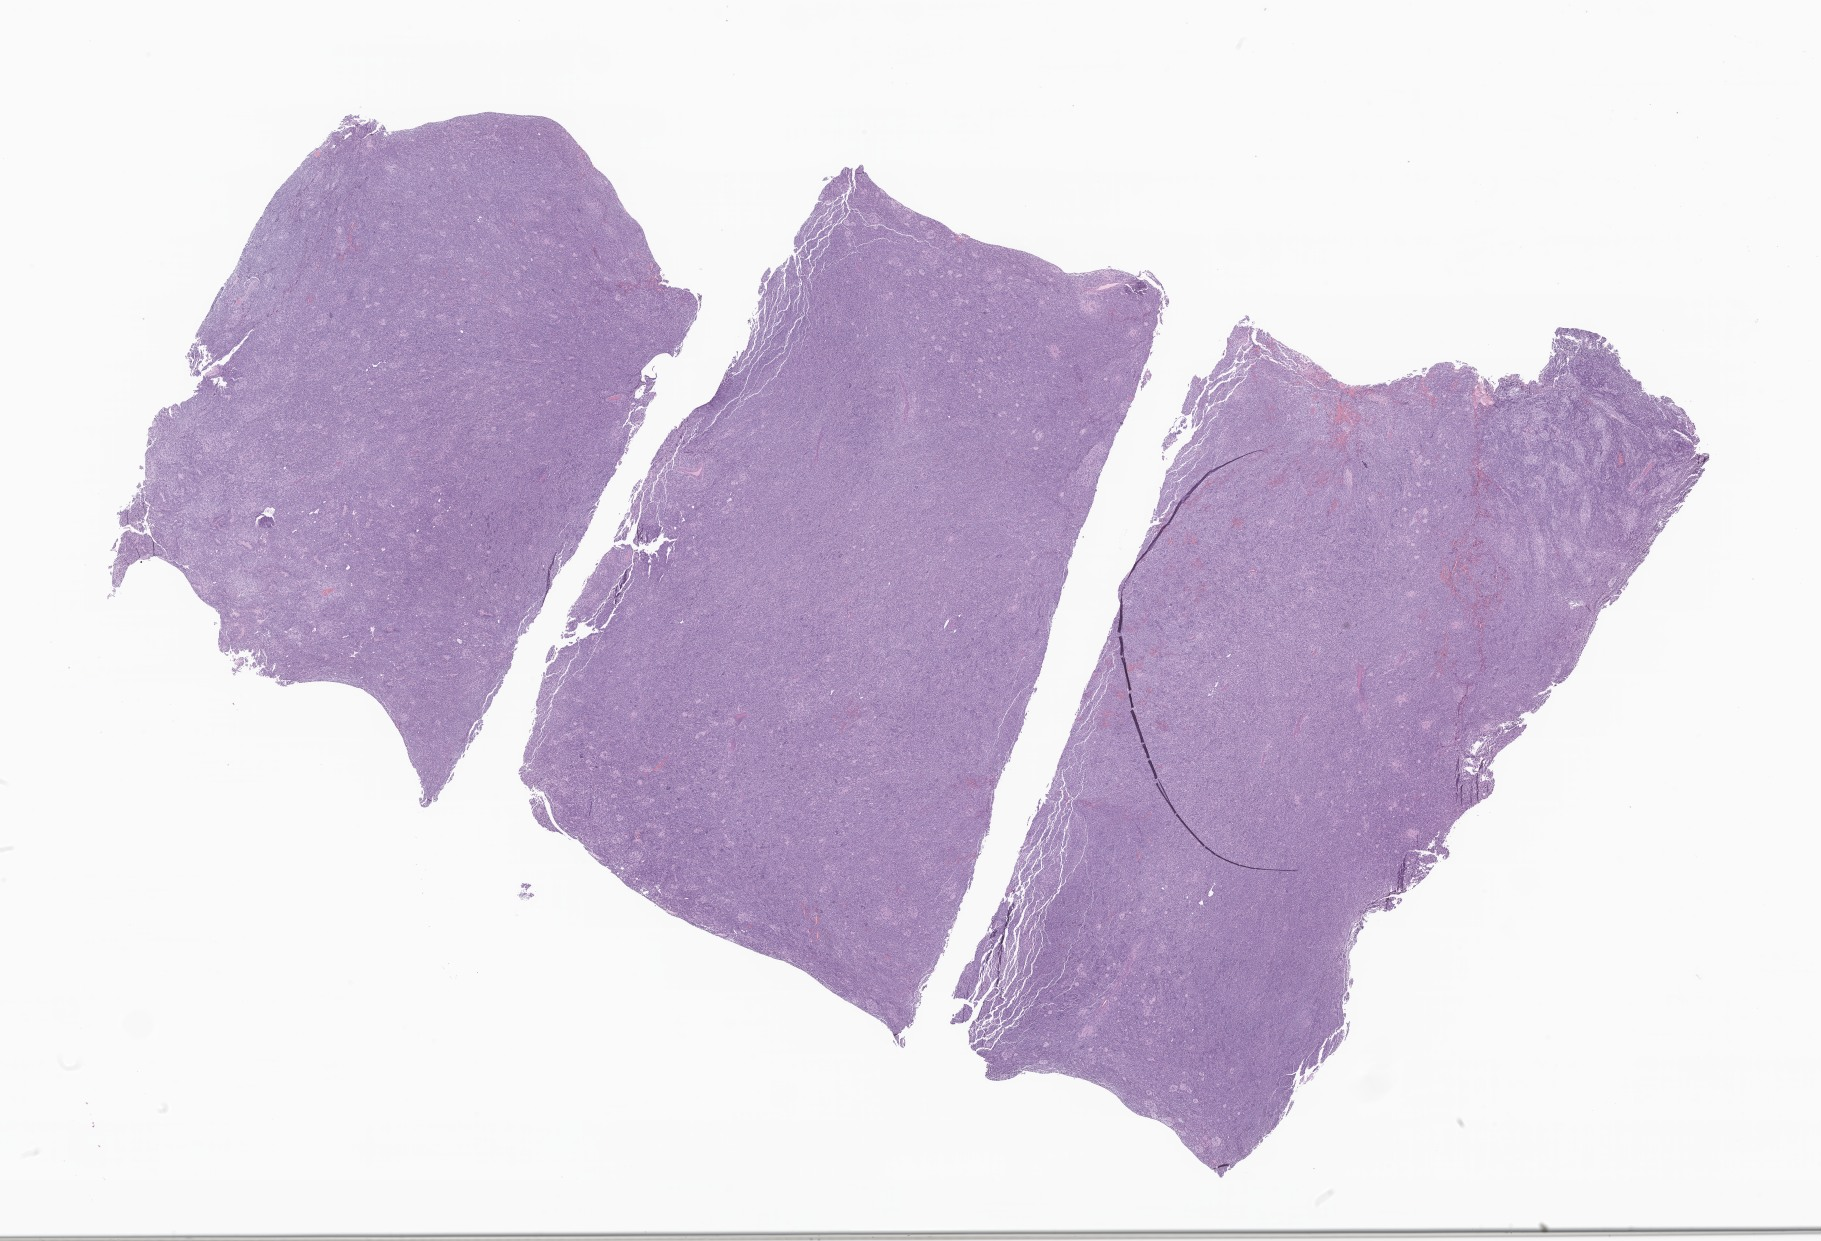
Whole-slide image, H&E stain of tumor tissue from the brain, shown as a low-resolution overview of the whole scanned area (about 30.7 x 20.9 mm); formalin-fixed paraffin-embedded section. Male patient, age 79 months (6 years 7 months).
Recorded diagnosis: Medulloblastoma, NOS.